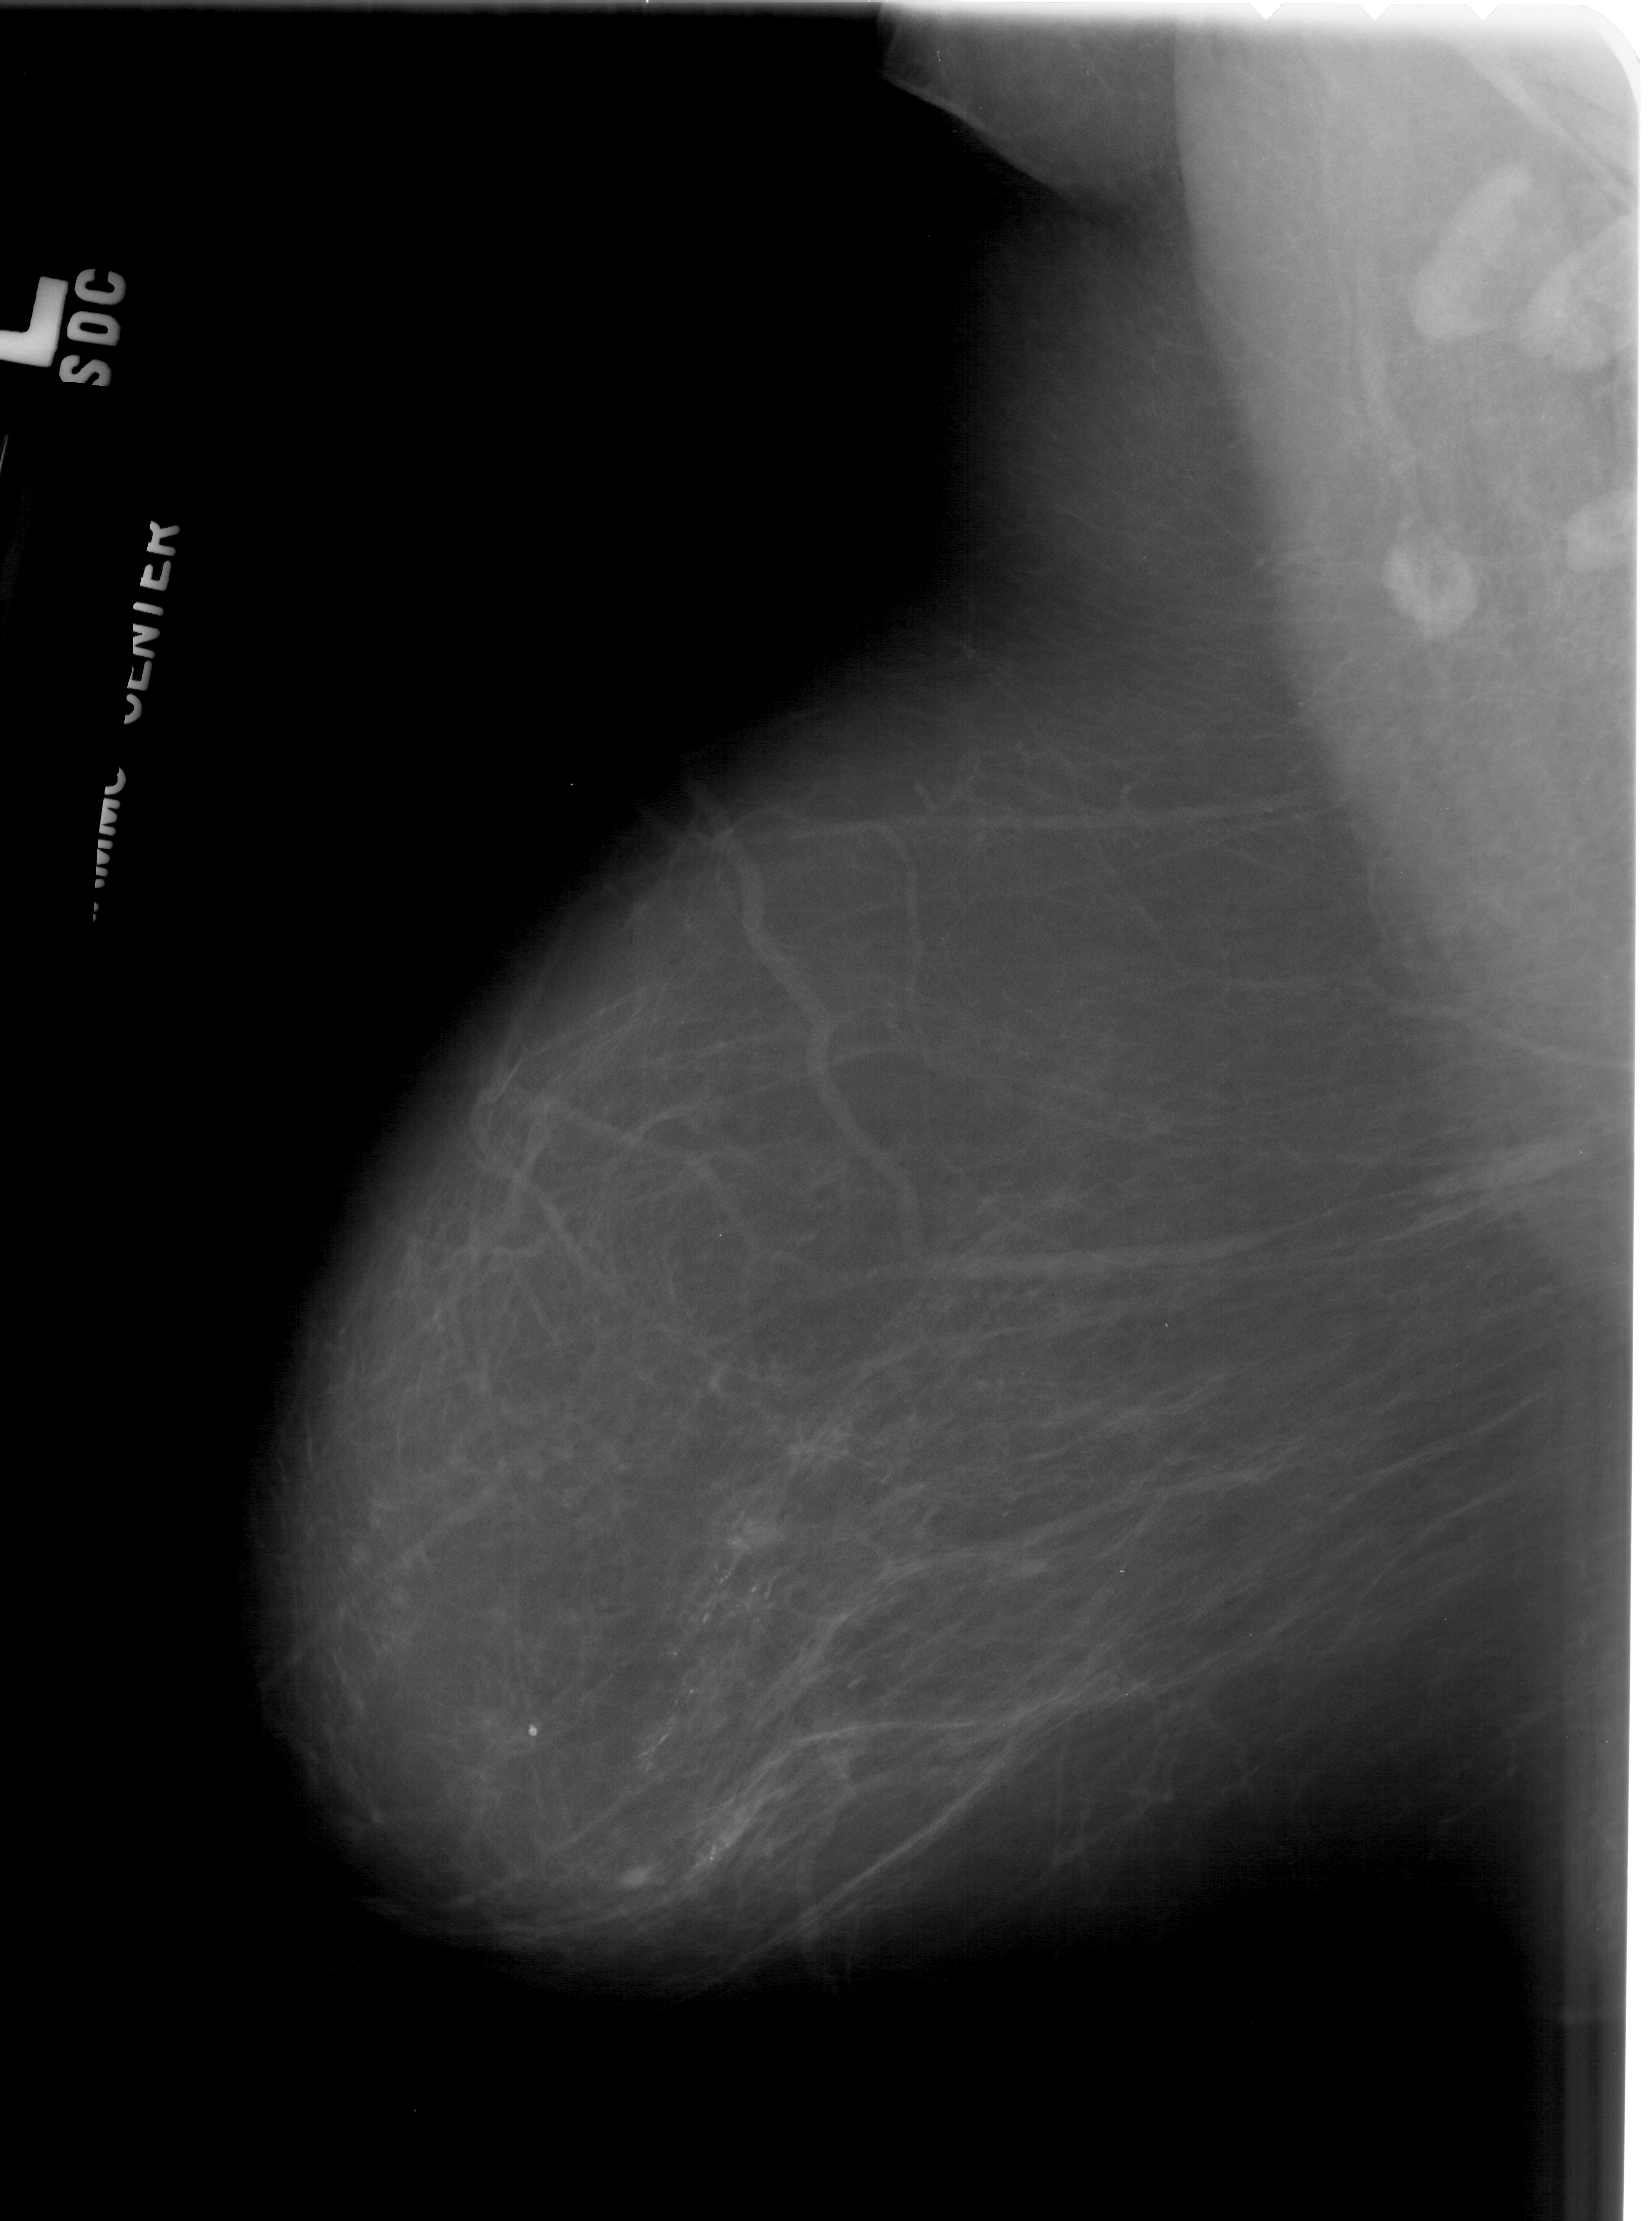
Digitized screen-film mammogram. Left breast. MLO view. Breast composition: scattered fibroglandular densities (BI-RADS density category 2 of 4). 1652 × 2221 image matrix.
Expert-marked regions of interest on this image (one box per marked abnormality):
- calcifications, morphology fine linear branching, distribution segmental; BI-RADS assessment category 5; pathology result (as recorded, not read from the image): malignant: bounding box <631,1398,947,1887> (left, top, right, bottom; pixels)